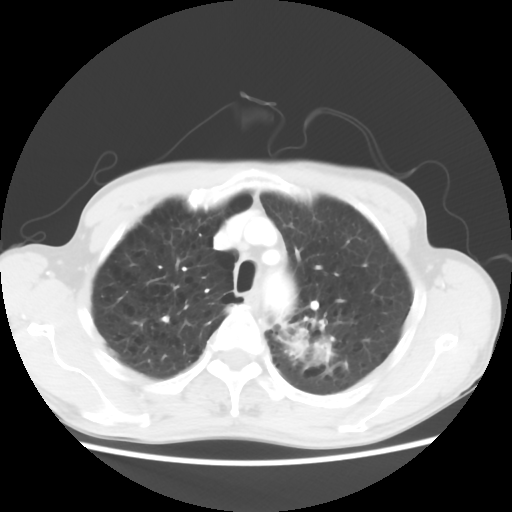
Chest CT, one axial slice; slice 50 of 64 in the series (ordered by position); reconstruction kernel STANDARD; 120 kVp; lung window (W 1500 / L -600 HU); 5 mm slice thickness; 512 × 512 image matrix. Patient: male, 63 years. Case-level facts recorded for this patient, not image findings: clinical TNM (as recorded): T2 N0 M0.
Outlined on this slice (bounding box drawn by a radiologist):
- lung tumour (recorded histology: adenocarcinoma): bounding box [x1, y1, x2, y2] px = [278, 329, 309, 359]